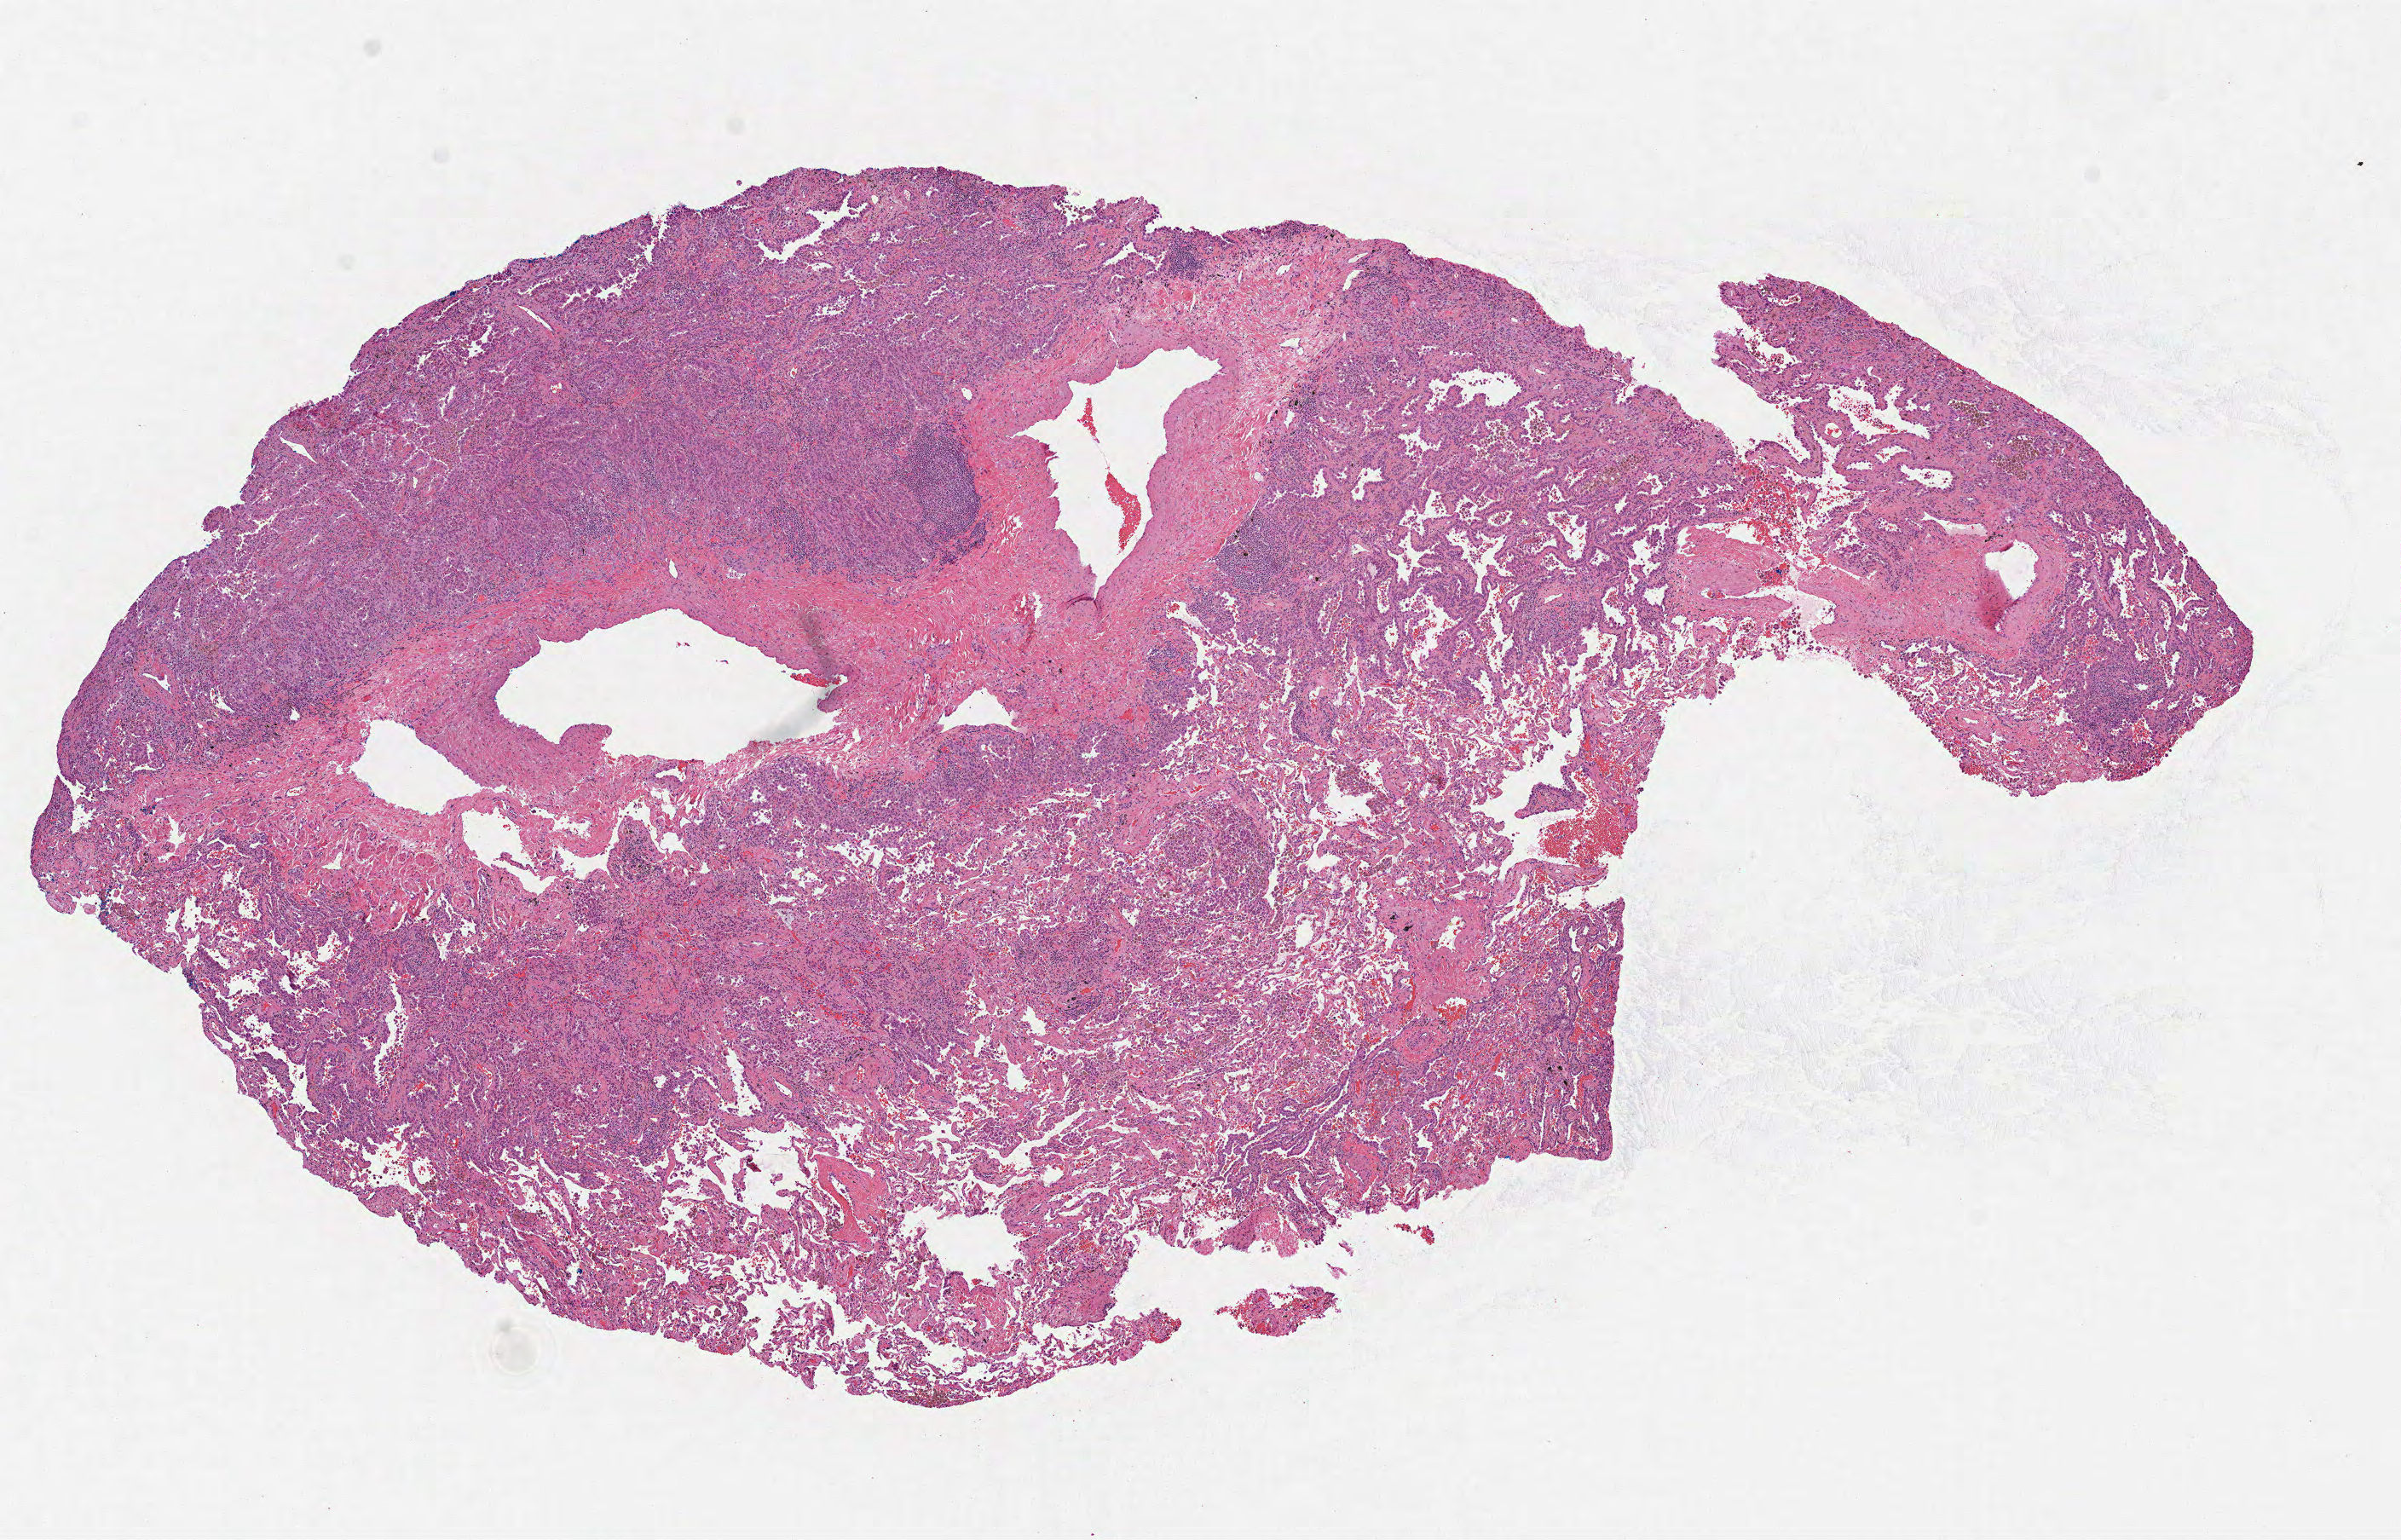
Digitized H&E-stained tissue section (whole slide) — a low-resolution overview of the entire scanned area, about 11.4 x 7.3 mm (from a 40x scan), formalin-fixed paraffin-embedded (FFPE) diagnostic section, sample: primary tumour, lung. Patient: male, age at initial diagnosis 54 years.
* diagnosis: Adenocarcinoma, NOS (upper lobe, lung)
* laterality: right
* AJCC pathologic stage: IB